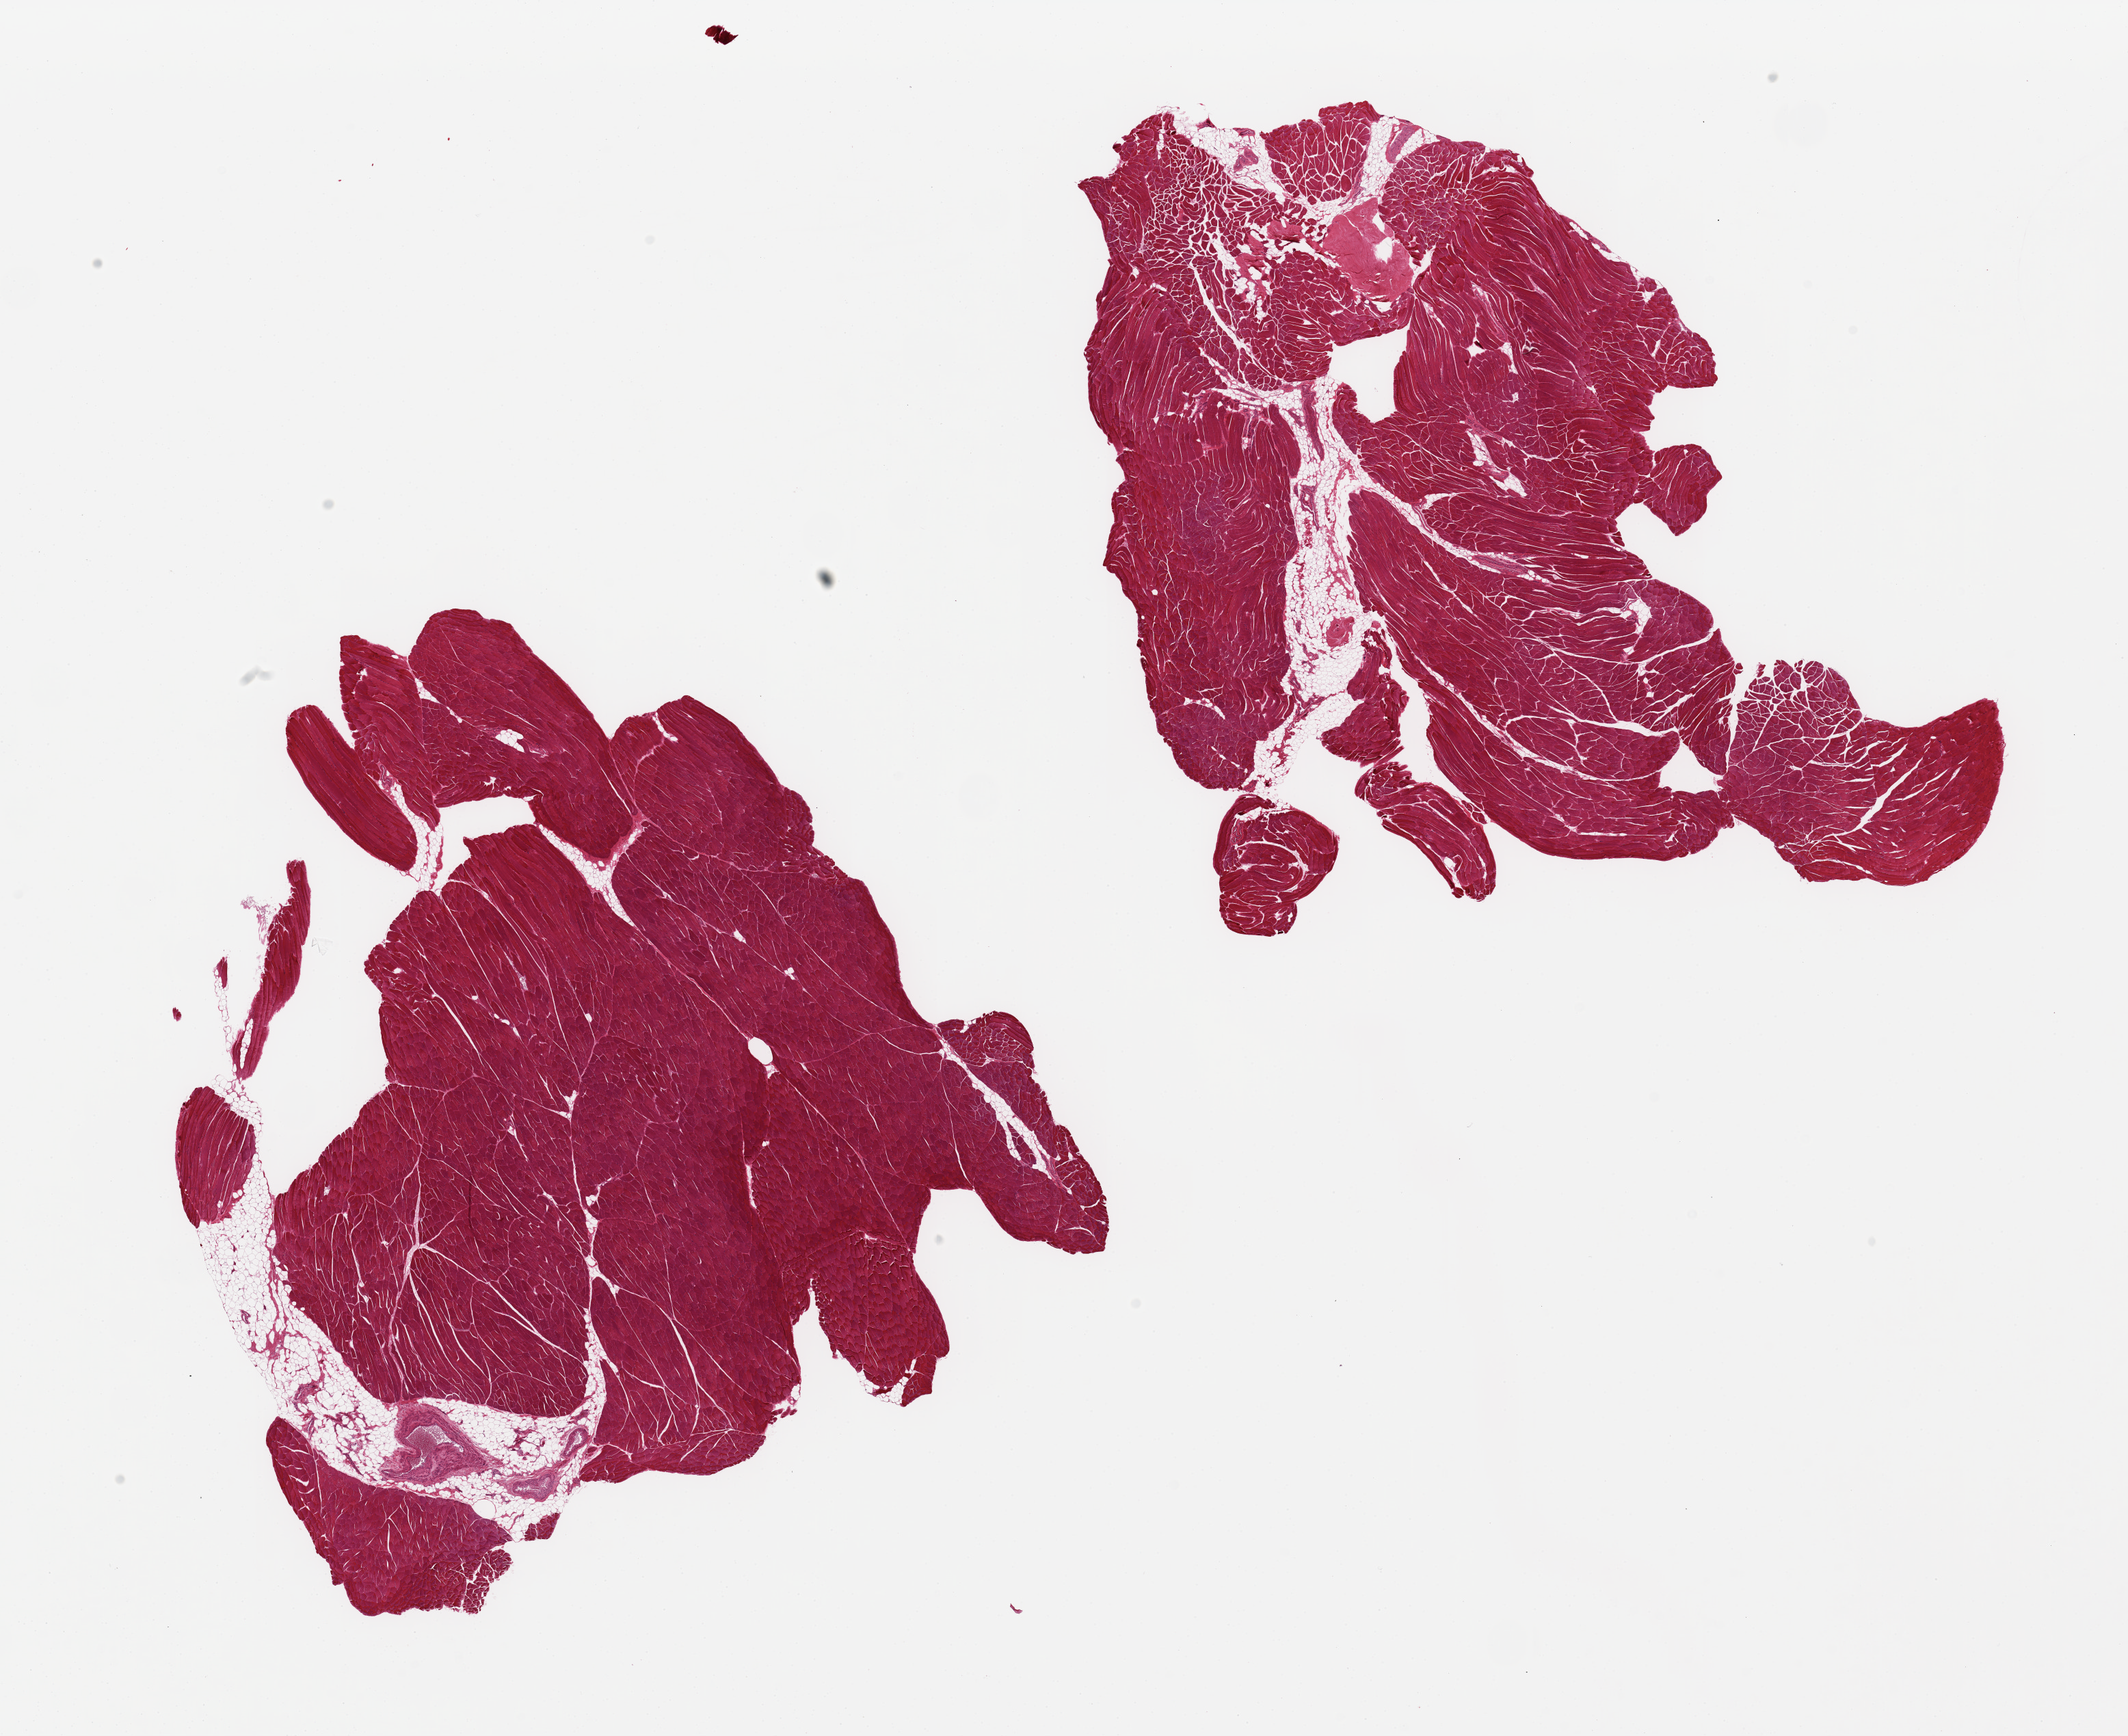
Whole-slide image, hematoxylin and eosin (H&E) stain, a low-resolution overview of the entire scanned area, about 24.6 x 20.1 mm (acquisition: 20x scan), PAXgene-fixed, paraffin-embedded tissue, section of skeletal muscle (target tissue), tissue donor sample. Male donor.
* pathologist's review note for this sample: 2 pieces; 1mm tendon in 1 piece; 10% internal fat in each piece